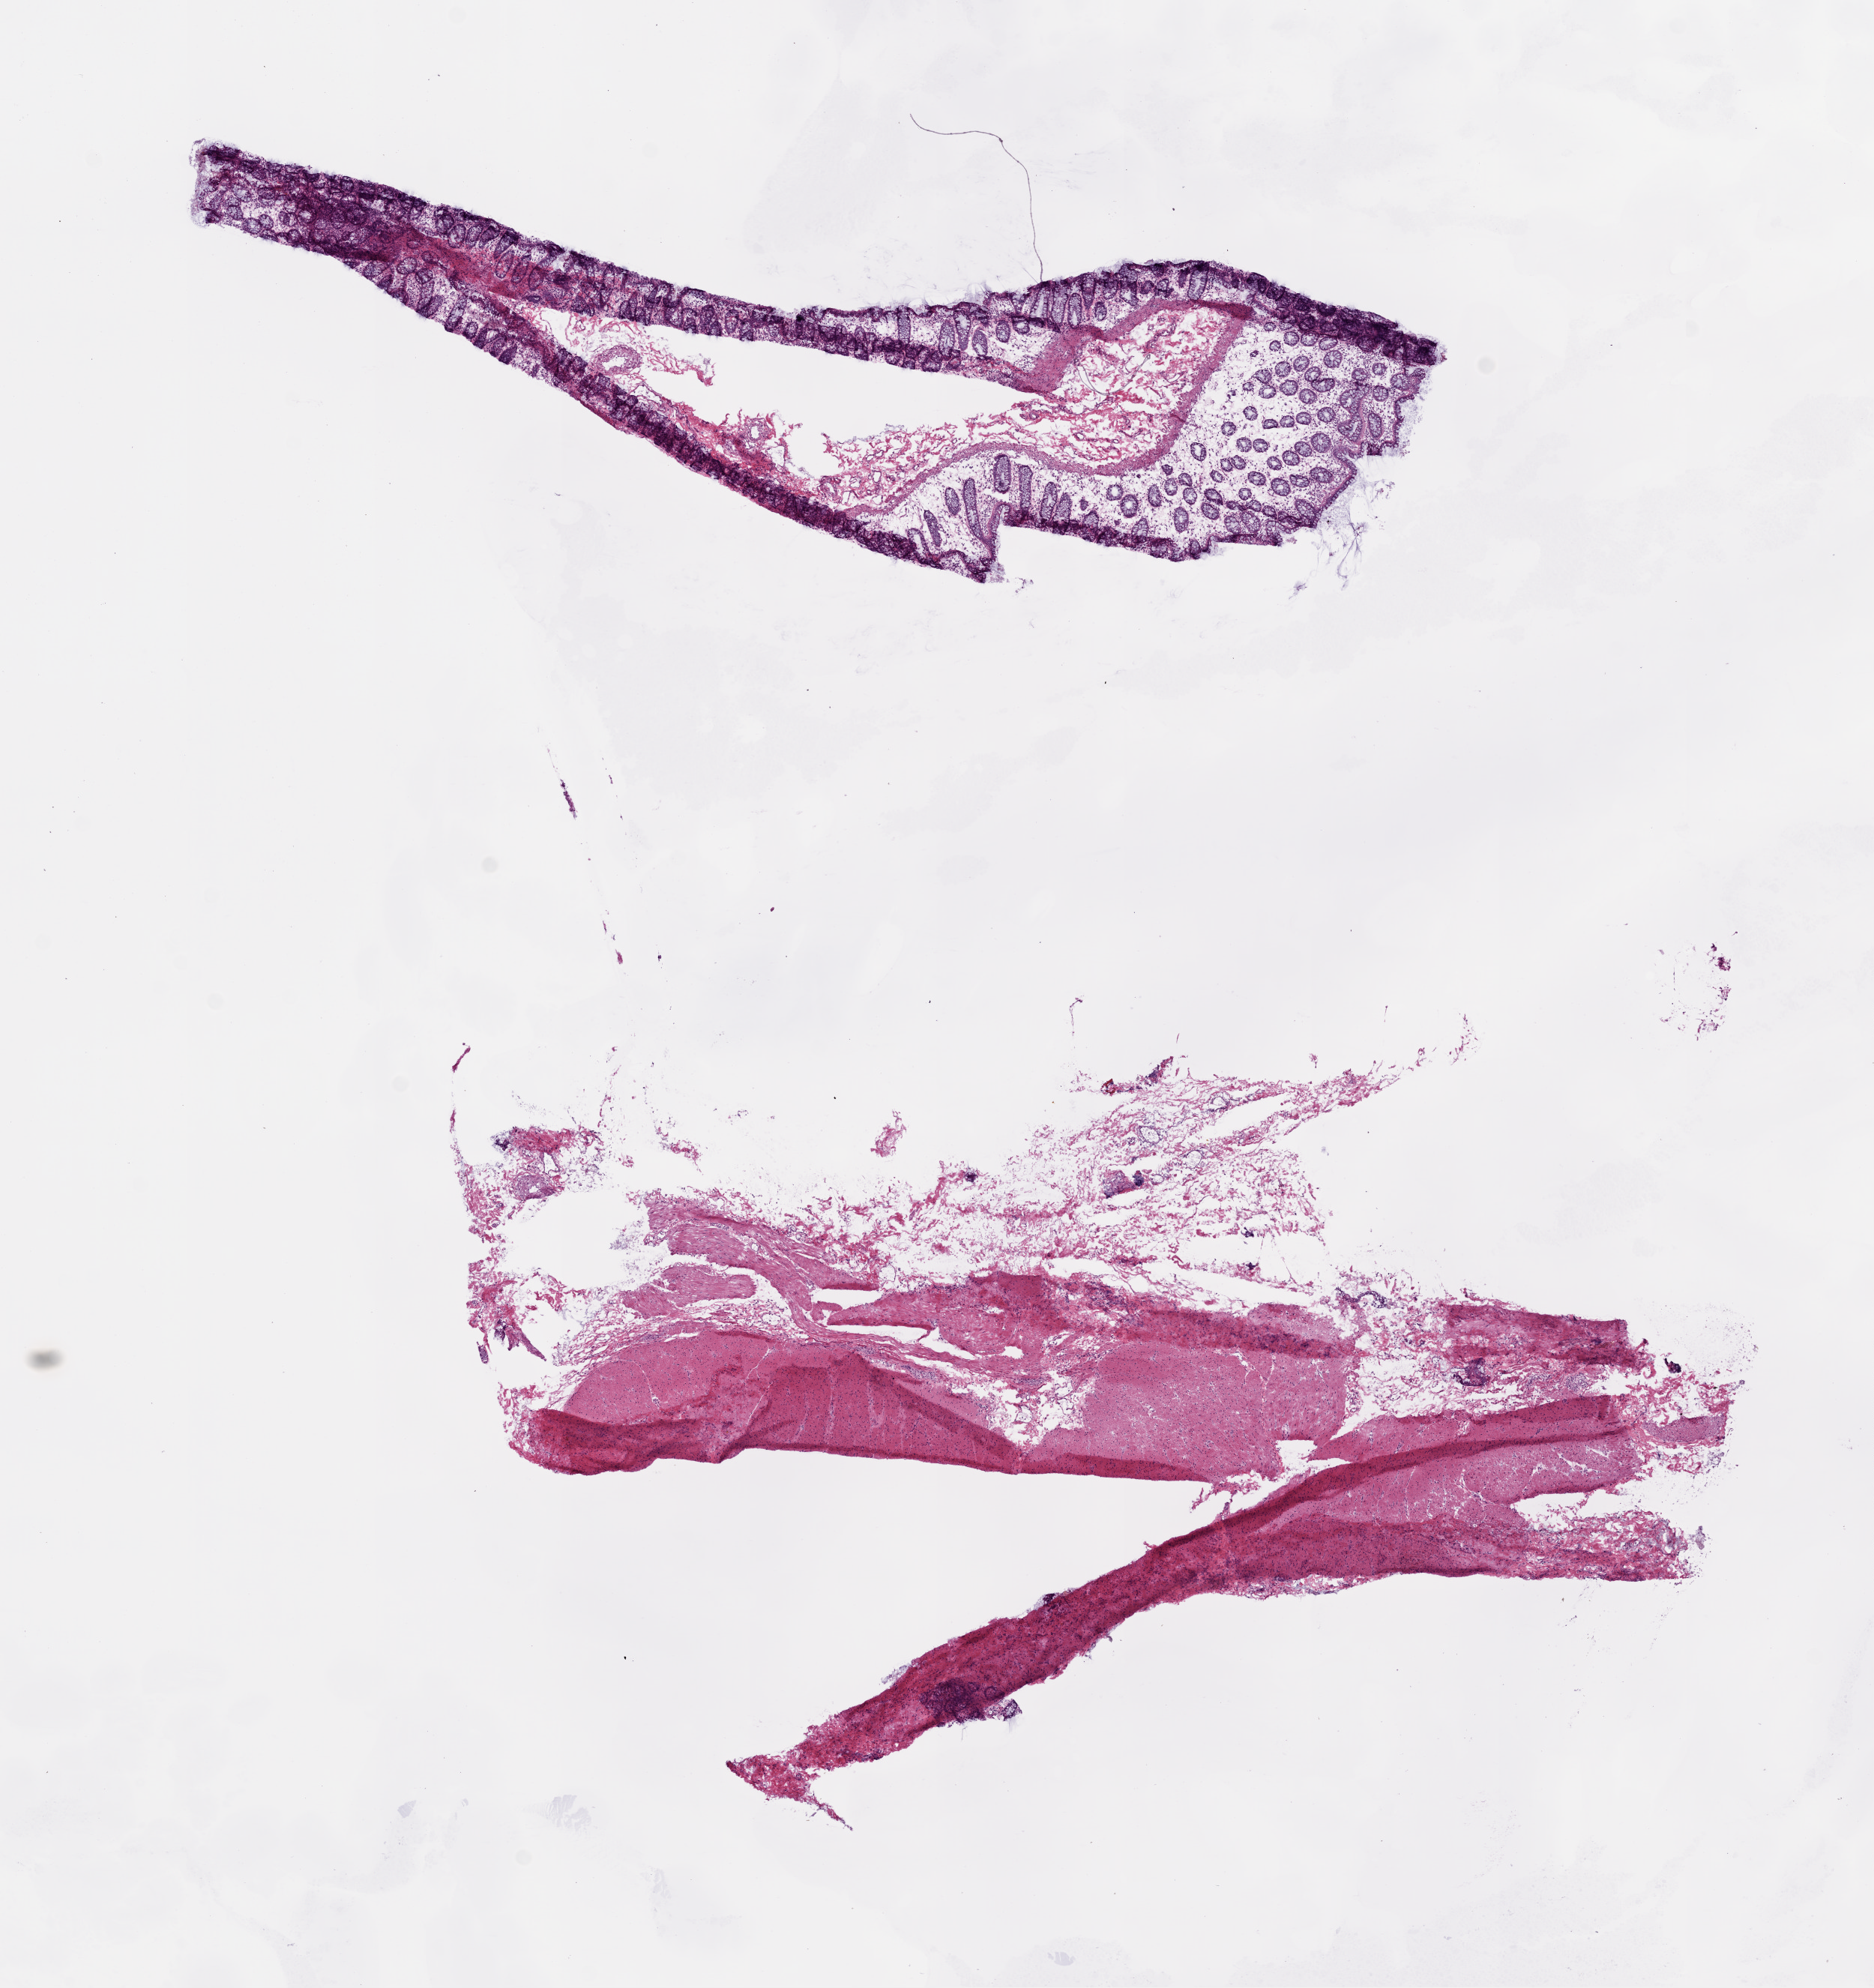
Whole-slide histology image, H&E-stained, shown as a low-resolution overview of the whole scanned area (about 10.0 x 10.6 mm, from a 20x scan); frozen section from the top of the tissue portion; solid tissue normal (non-tumour tissue) sample from the colon. Patient: male, age at initial diagnosis 78 years.
This section: solid tissue normal (non-tumour) sample from the same patient. Patient diagnosis: Adenocarcinoma, NOS.